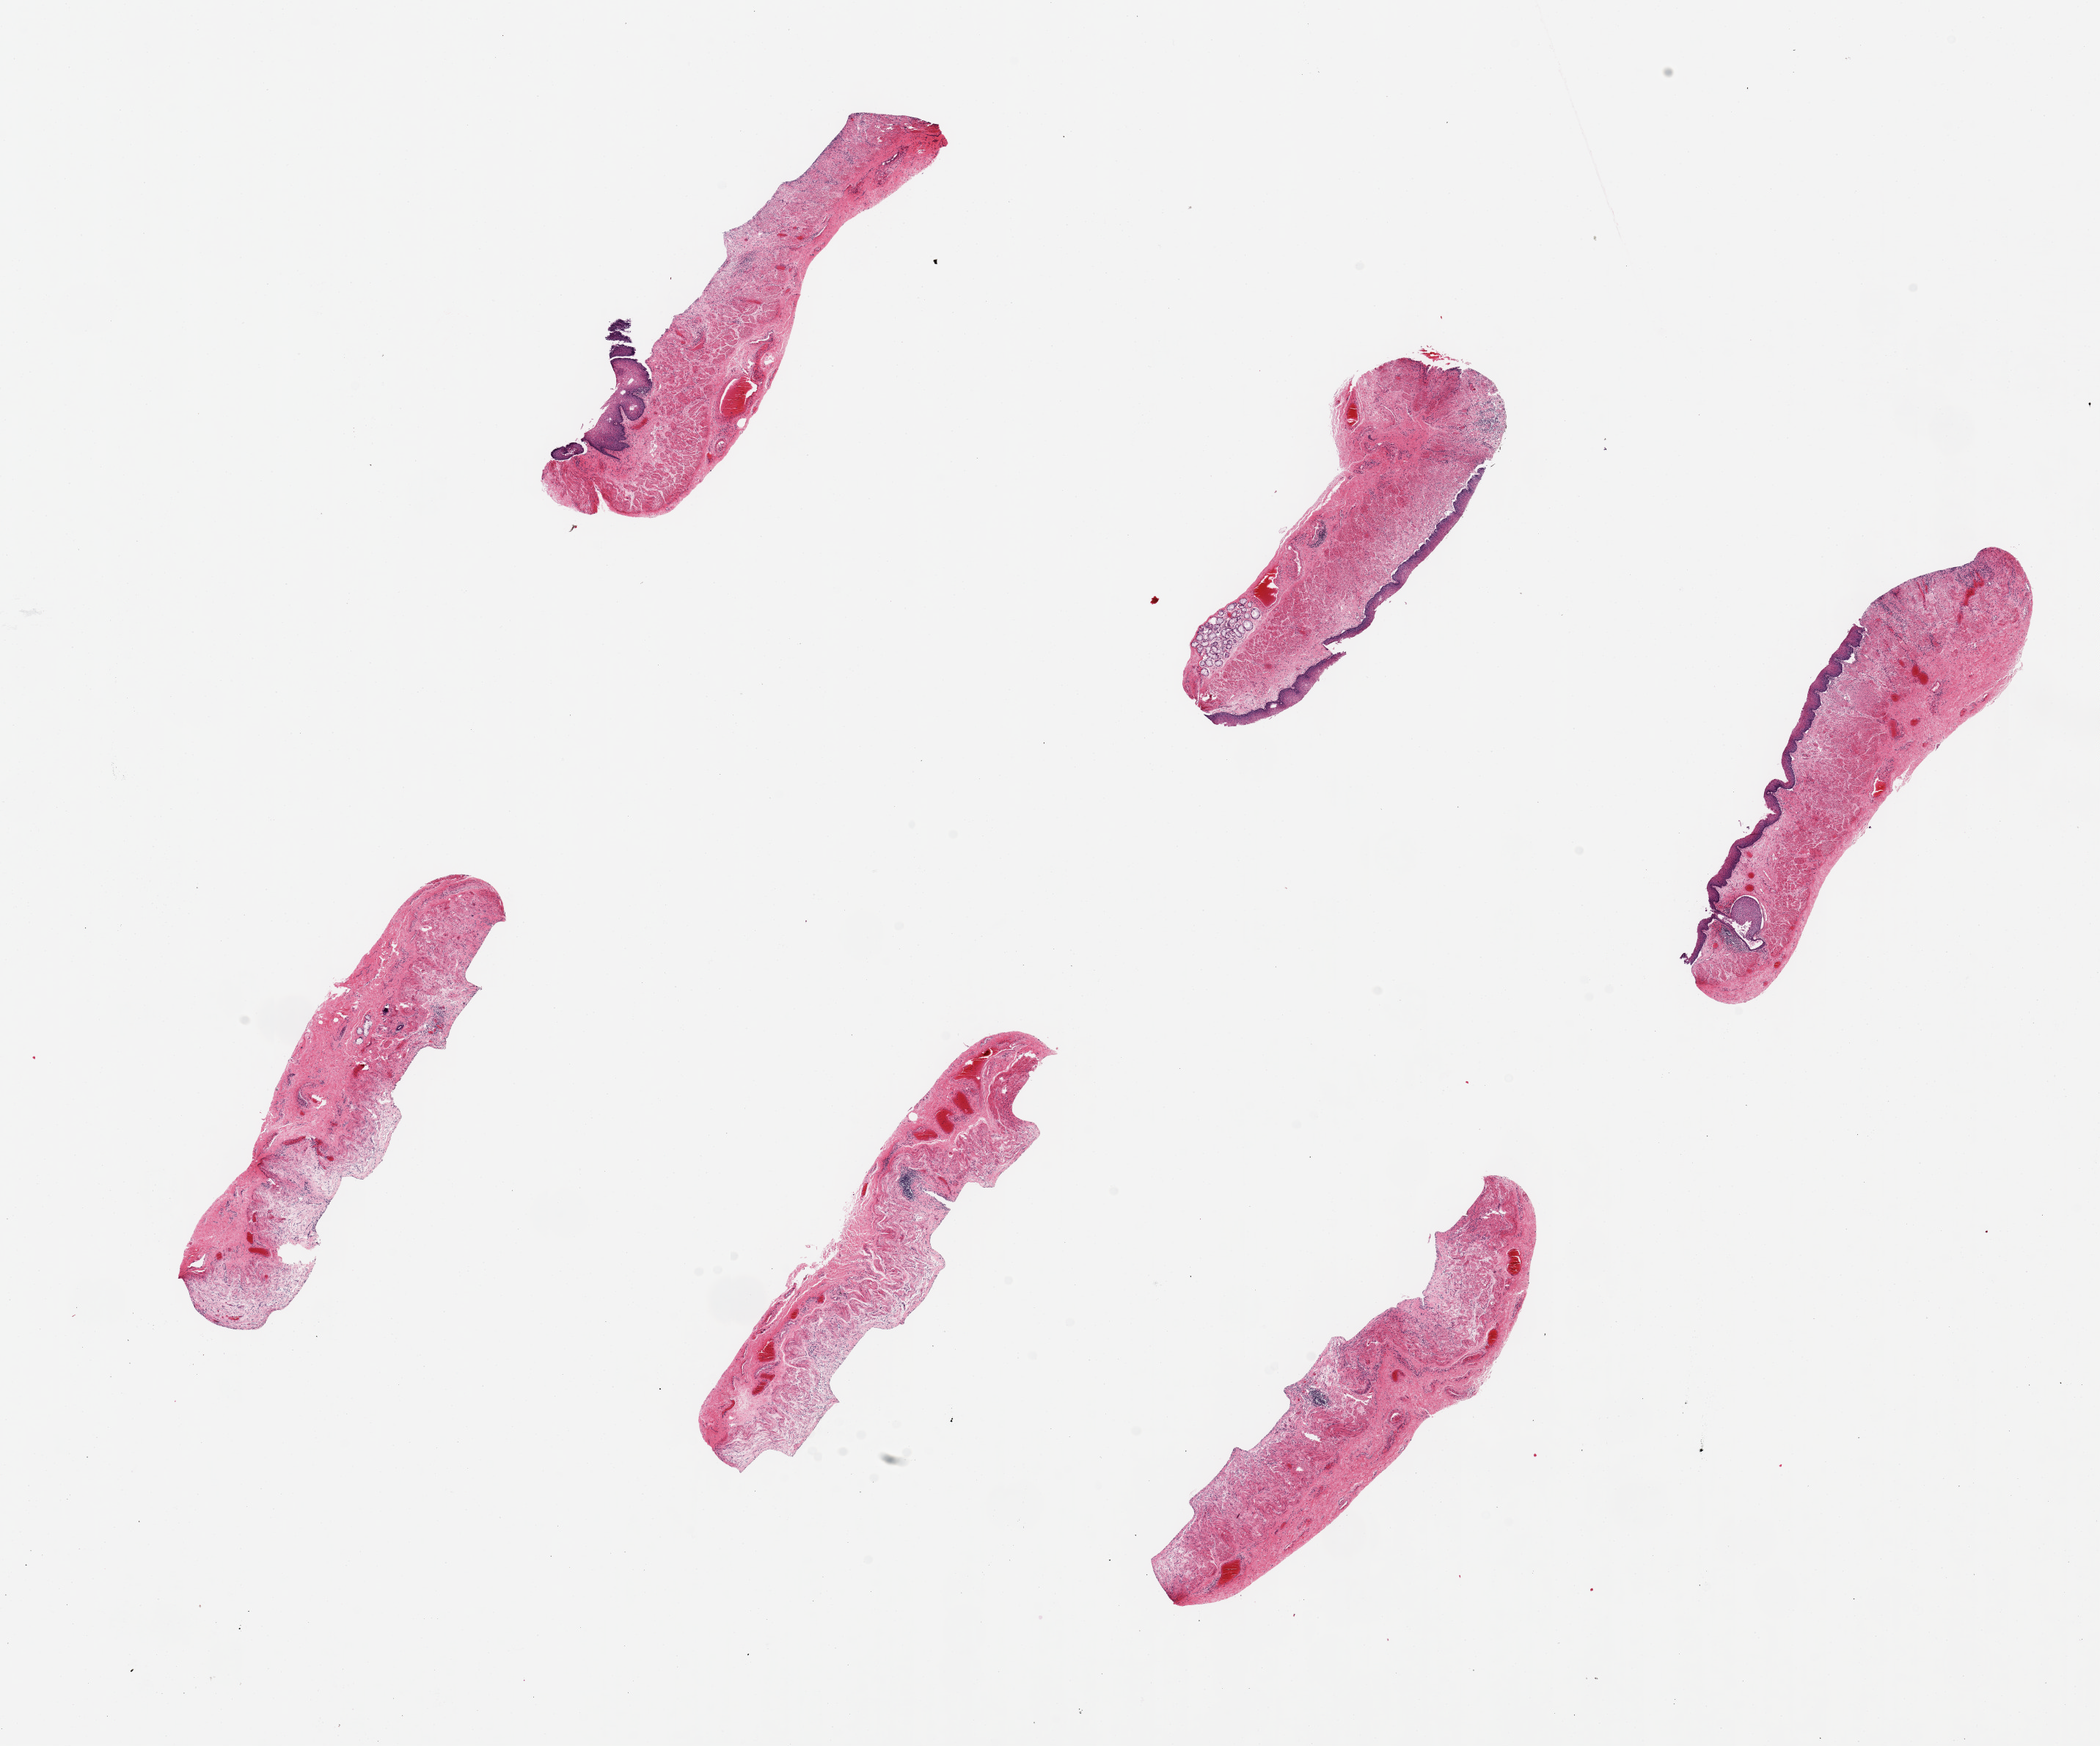
Digitized haematoxylin and eosin-stained section, shown as a low-resolution overview of the whole scanned area (about 22.6 x 18.8 mm, from a 20x scan). PAXgene-fixed, paraffin-embedded tissue. Section of esophageal mucous membrane (target tissue). Tissue donor sample. Donor sex: male.
* reviewer comment on this tissue sample: 6 pieces ~6x1.5mm, mucosa sloughed entirely on 3, partly on two; where visible, ~10% of thickness